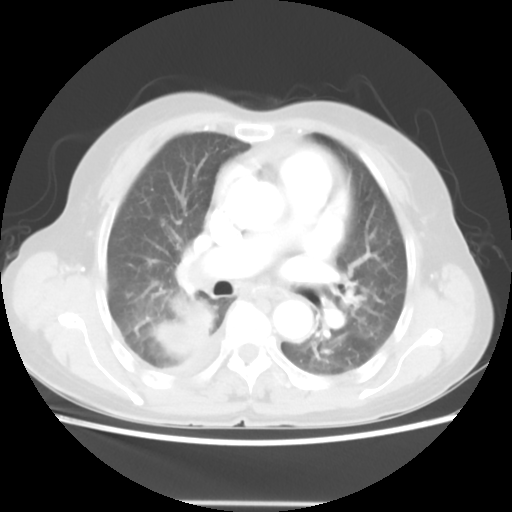
Chest CT, one axial slice; slice 29 of 52 in the series (ordered by position); reconstruction kernel STANDARD; 140 kVp; lung window (W 1500 / L -600 HU); 512 × 512 image matrix, field of view 337 × 337 mm. Female patient, age 67 years. Case-level facts recorded for this patient, not image findings: clinical TNM (as recorded): T3 N1 M1.
Annotated regions visible in this slice (rectangle marked by the reading radiologist):
- lung tumour (recorded histology: adenocarcinoma): box from (x=152, y=292) to (x=216, y=362) px